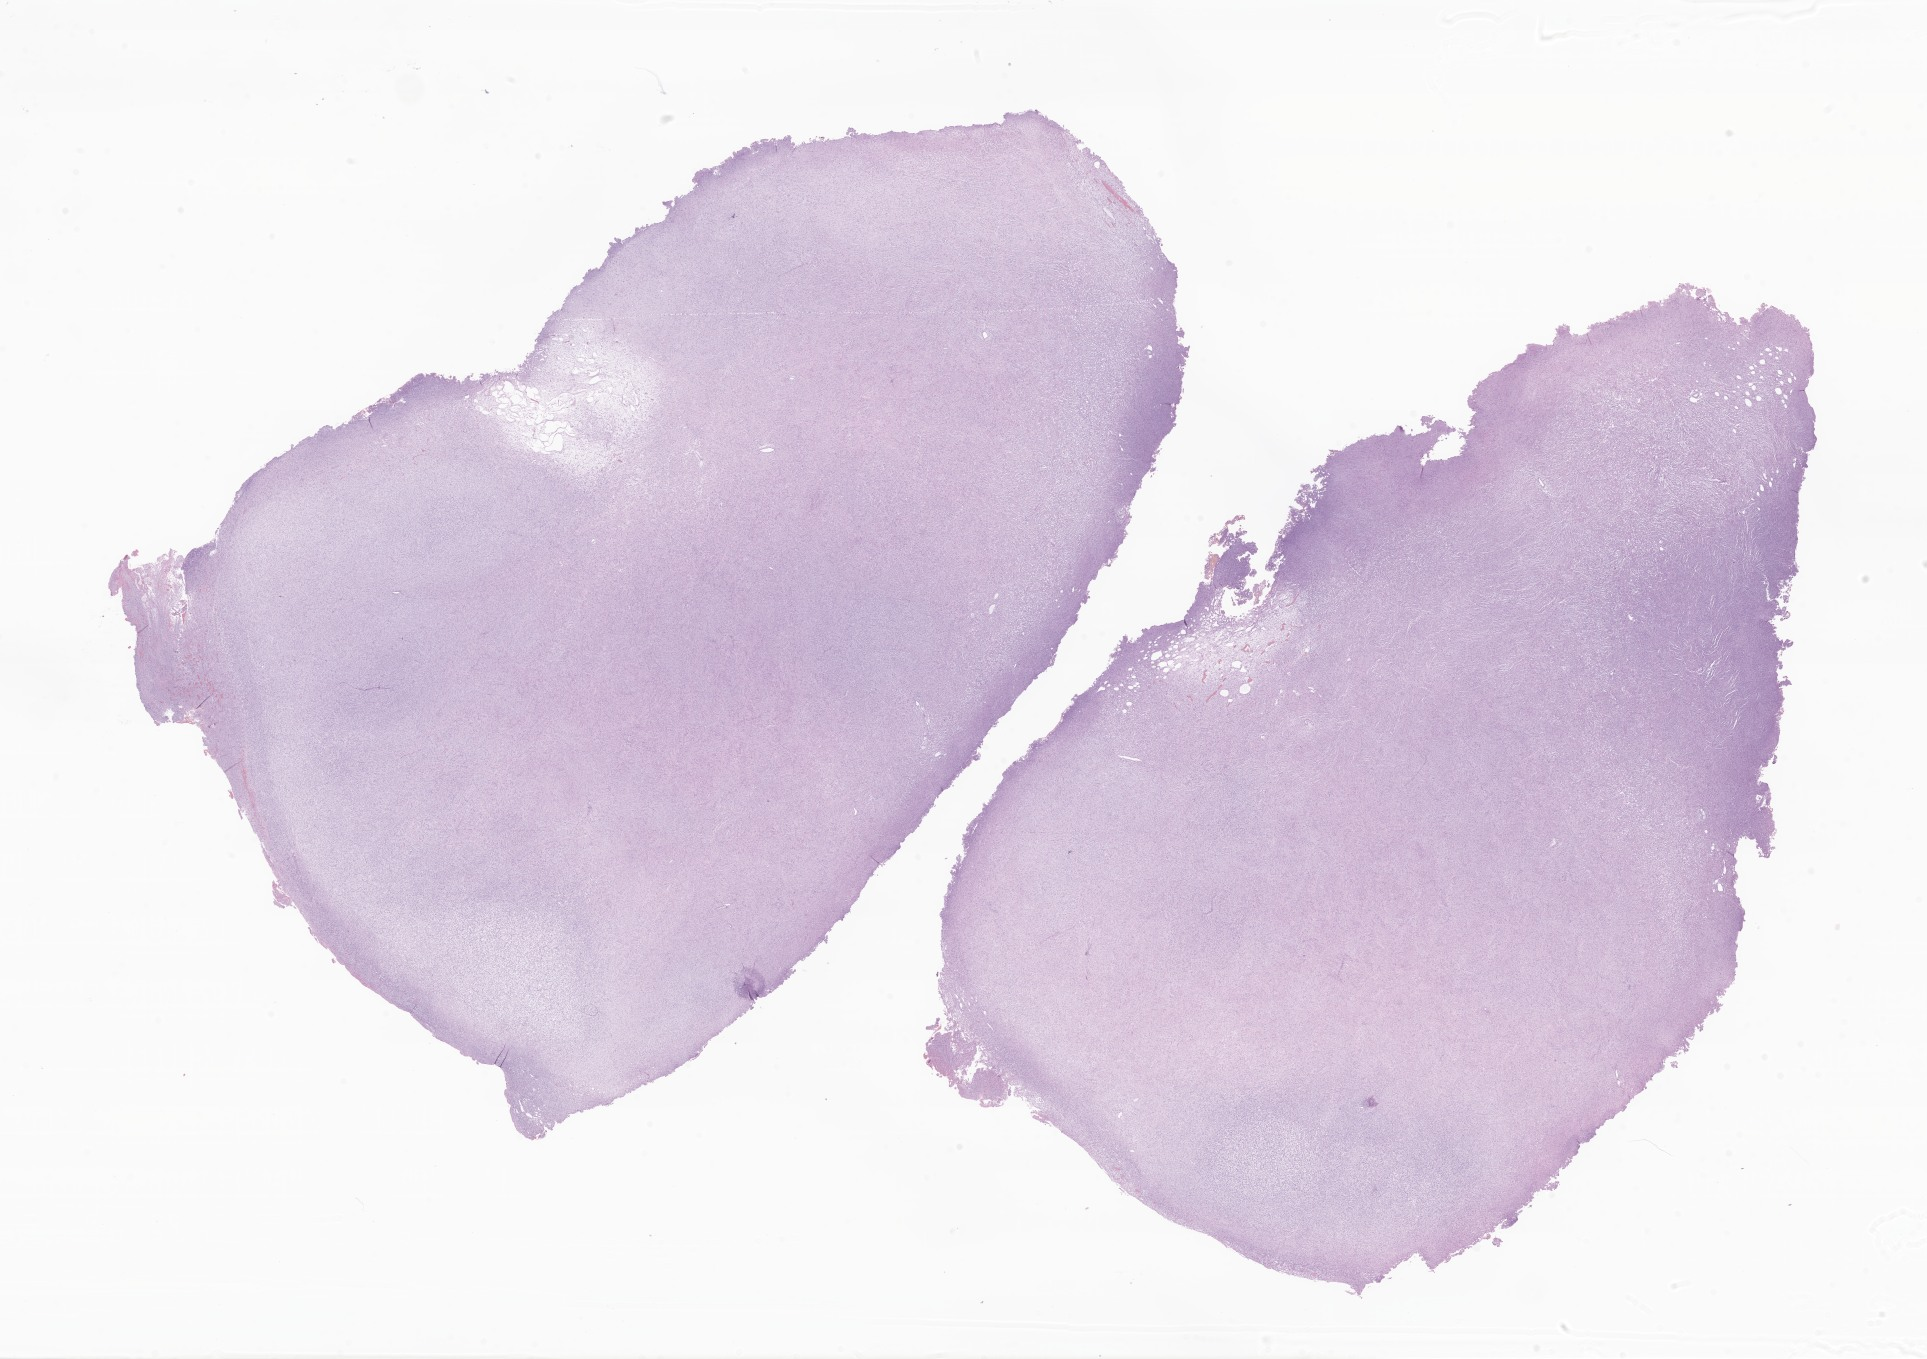
Hematoxylin and eosin (H&E) whole-slide image of tumor tissue from the brain, low-resolution overview of the scanned area, about 32.5 x 22.9 mm, formalin-fixed paraffin-embedded section. Male patient, age 77 days.
Diagnosis (ICD-O-3 morphology term): Neoplasm, uncertain whether benign or malignant.